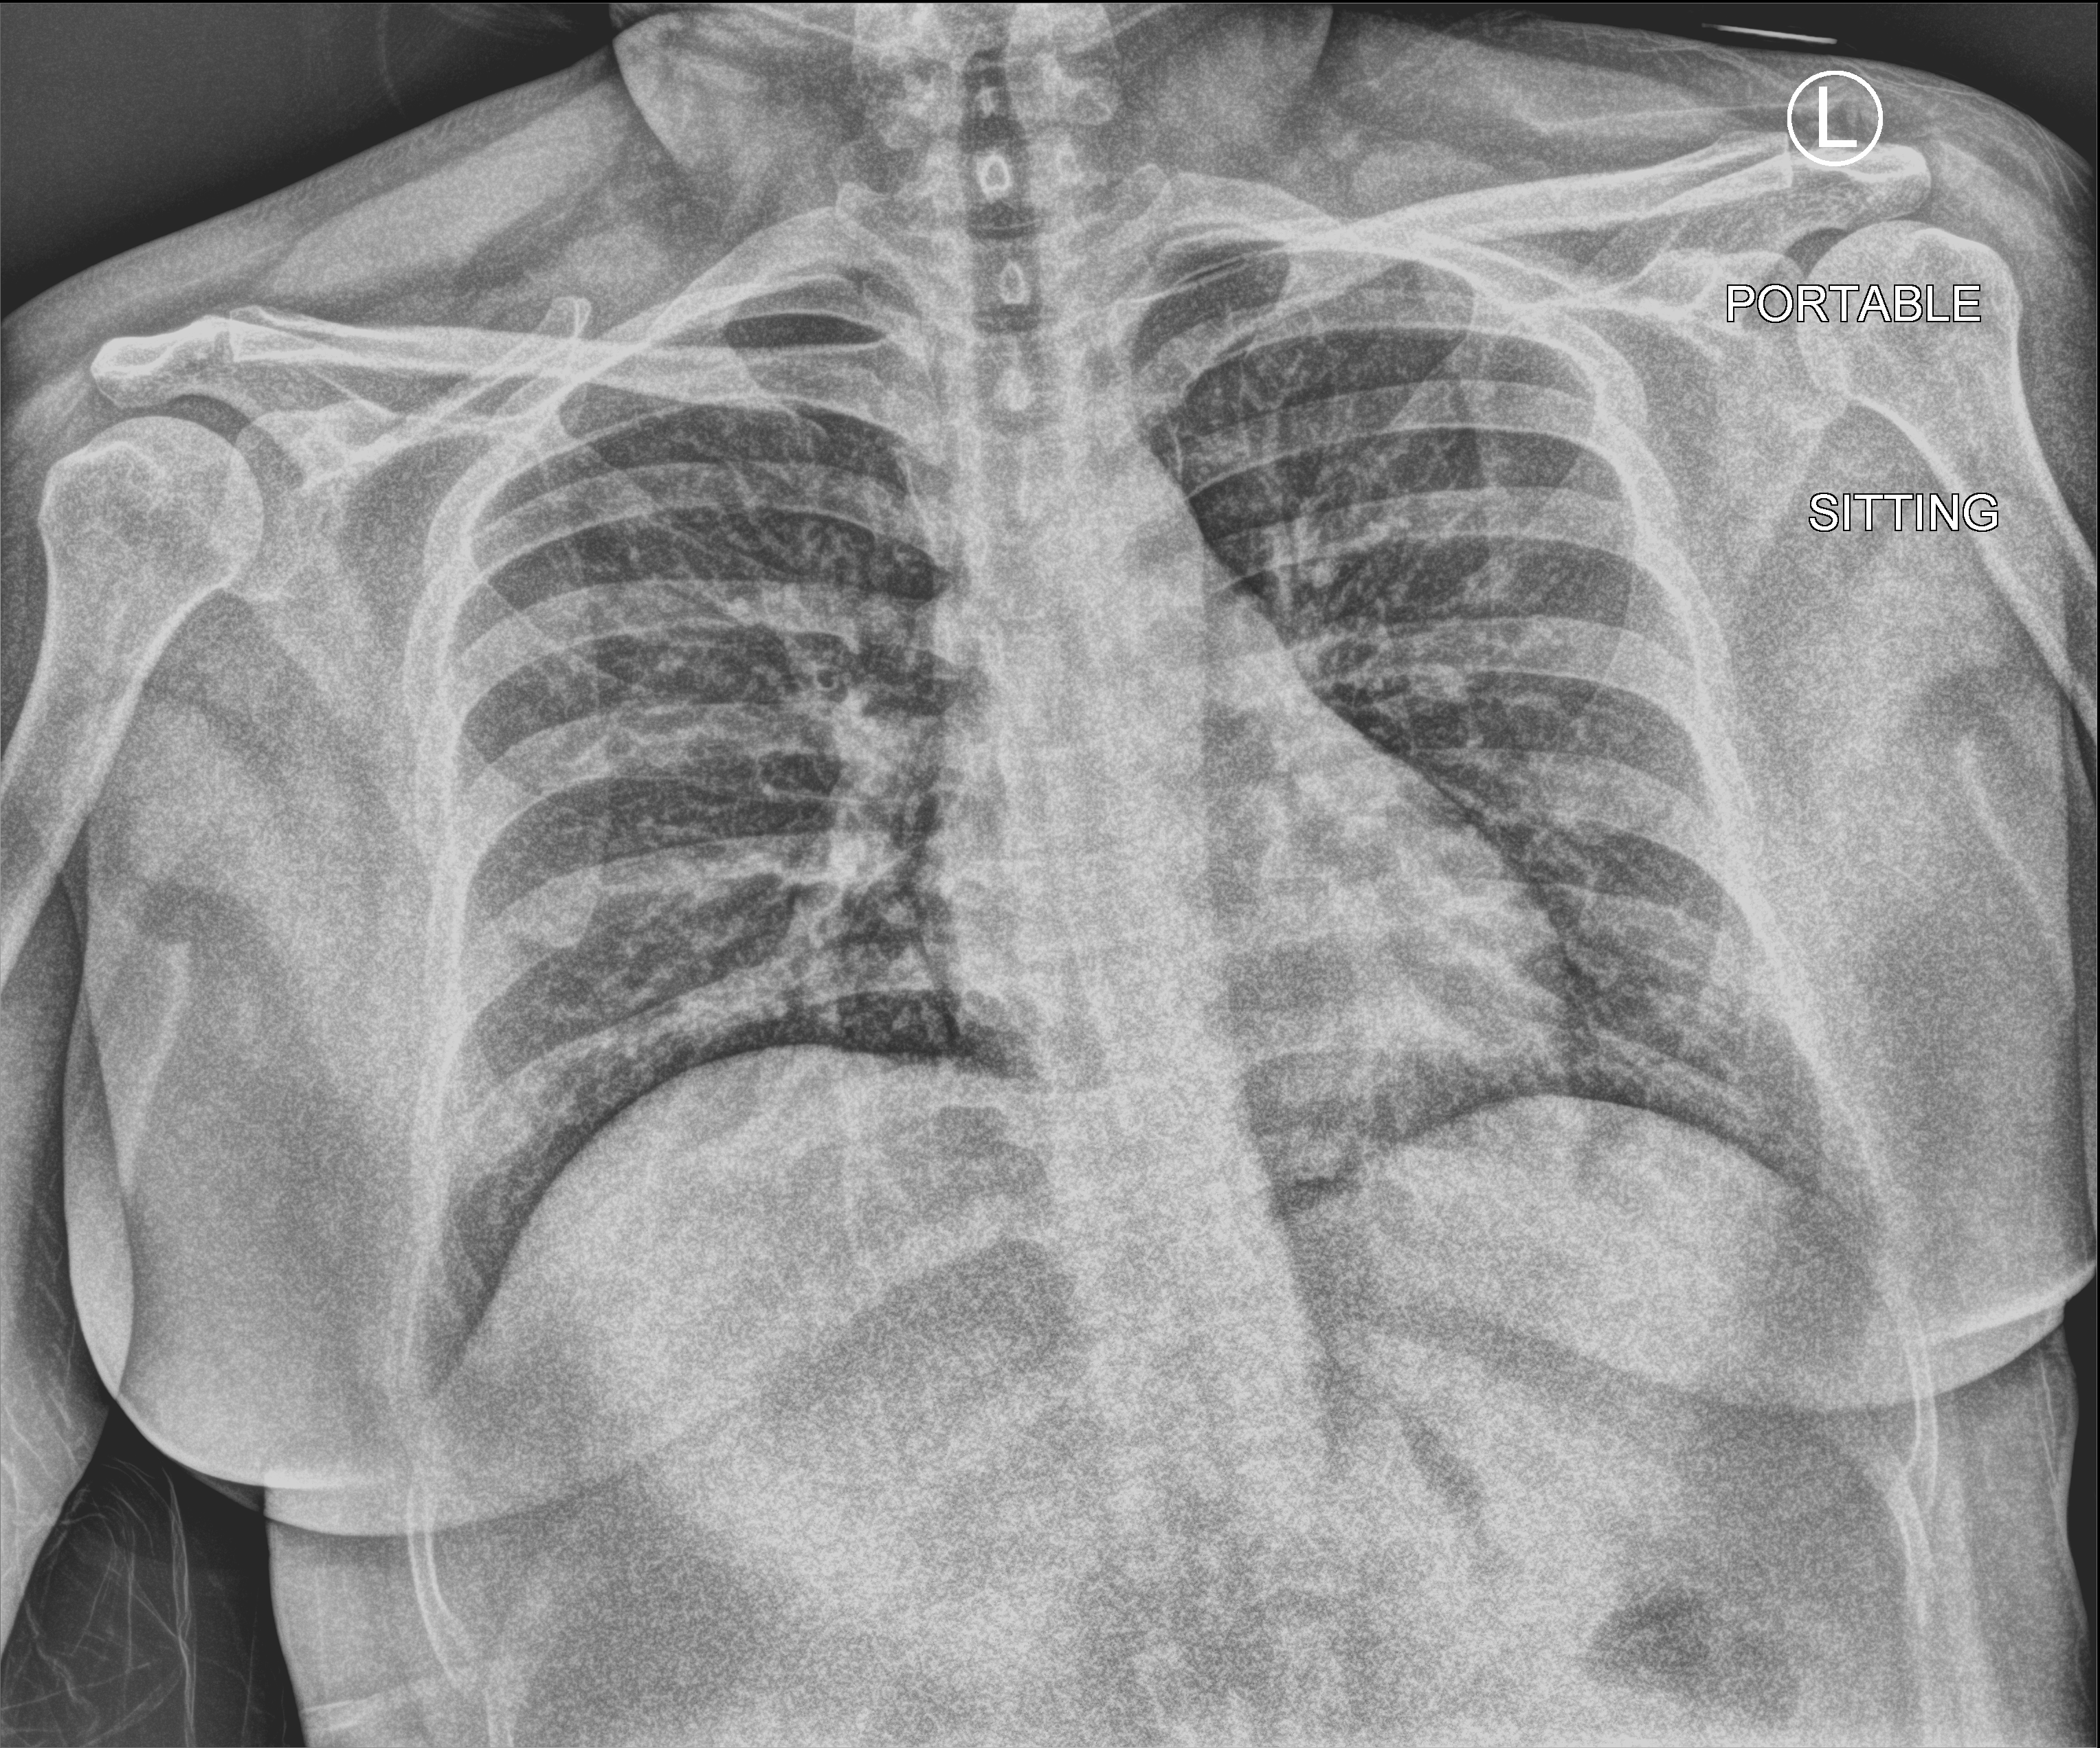
Chest X-ray (portable), anteroposterior (AP) projection. Patient hospitalised with COVID-19; female, aged 18–59 years.
From the hospital-stay record, not from the radiograph (when in the stay this image was taken is not recorded):
- admitted to intensive care during this hospital stay: no
- mechanically ventilated during this hospital stay: no